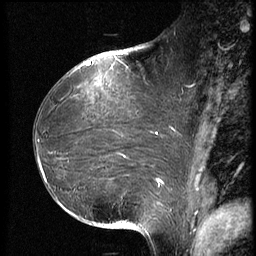
Breast MRI (dynamic contrast-enhanced), one sagittal slice. Position 36 of 66 along the scan axis. Dynamic contrast-enhanced series, image 2 of 3 at this slice position (ordered by acquisition). 1.5 T. TE 4.2 ms, TR 8.9 ms. 2.5 mm slice thickness. 256 × 256 image matrix, field of view 200 × 200 mm. Female patient, age 39 years. From the clinical record (not read from this slice): setting: breast cancer imaged before/during neoadjuvant chemotherapy; receptor status: HER2-positive.
Structures marked on this image (semi-automatic segmentation, software-assisted and operator-edited):
- analysis volume of interest (the breast-tissue region the enhancement analysis was run in; not a lesion): bounding box <32,75,188,218> (left, top, right, bottom; pixels)
- tumour enhancement mask (voxels above the 140 % enhancement threshold inside the analysis volume of interest): <38,133,158,184>